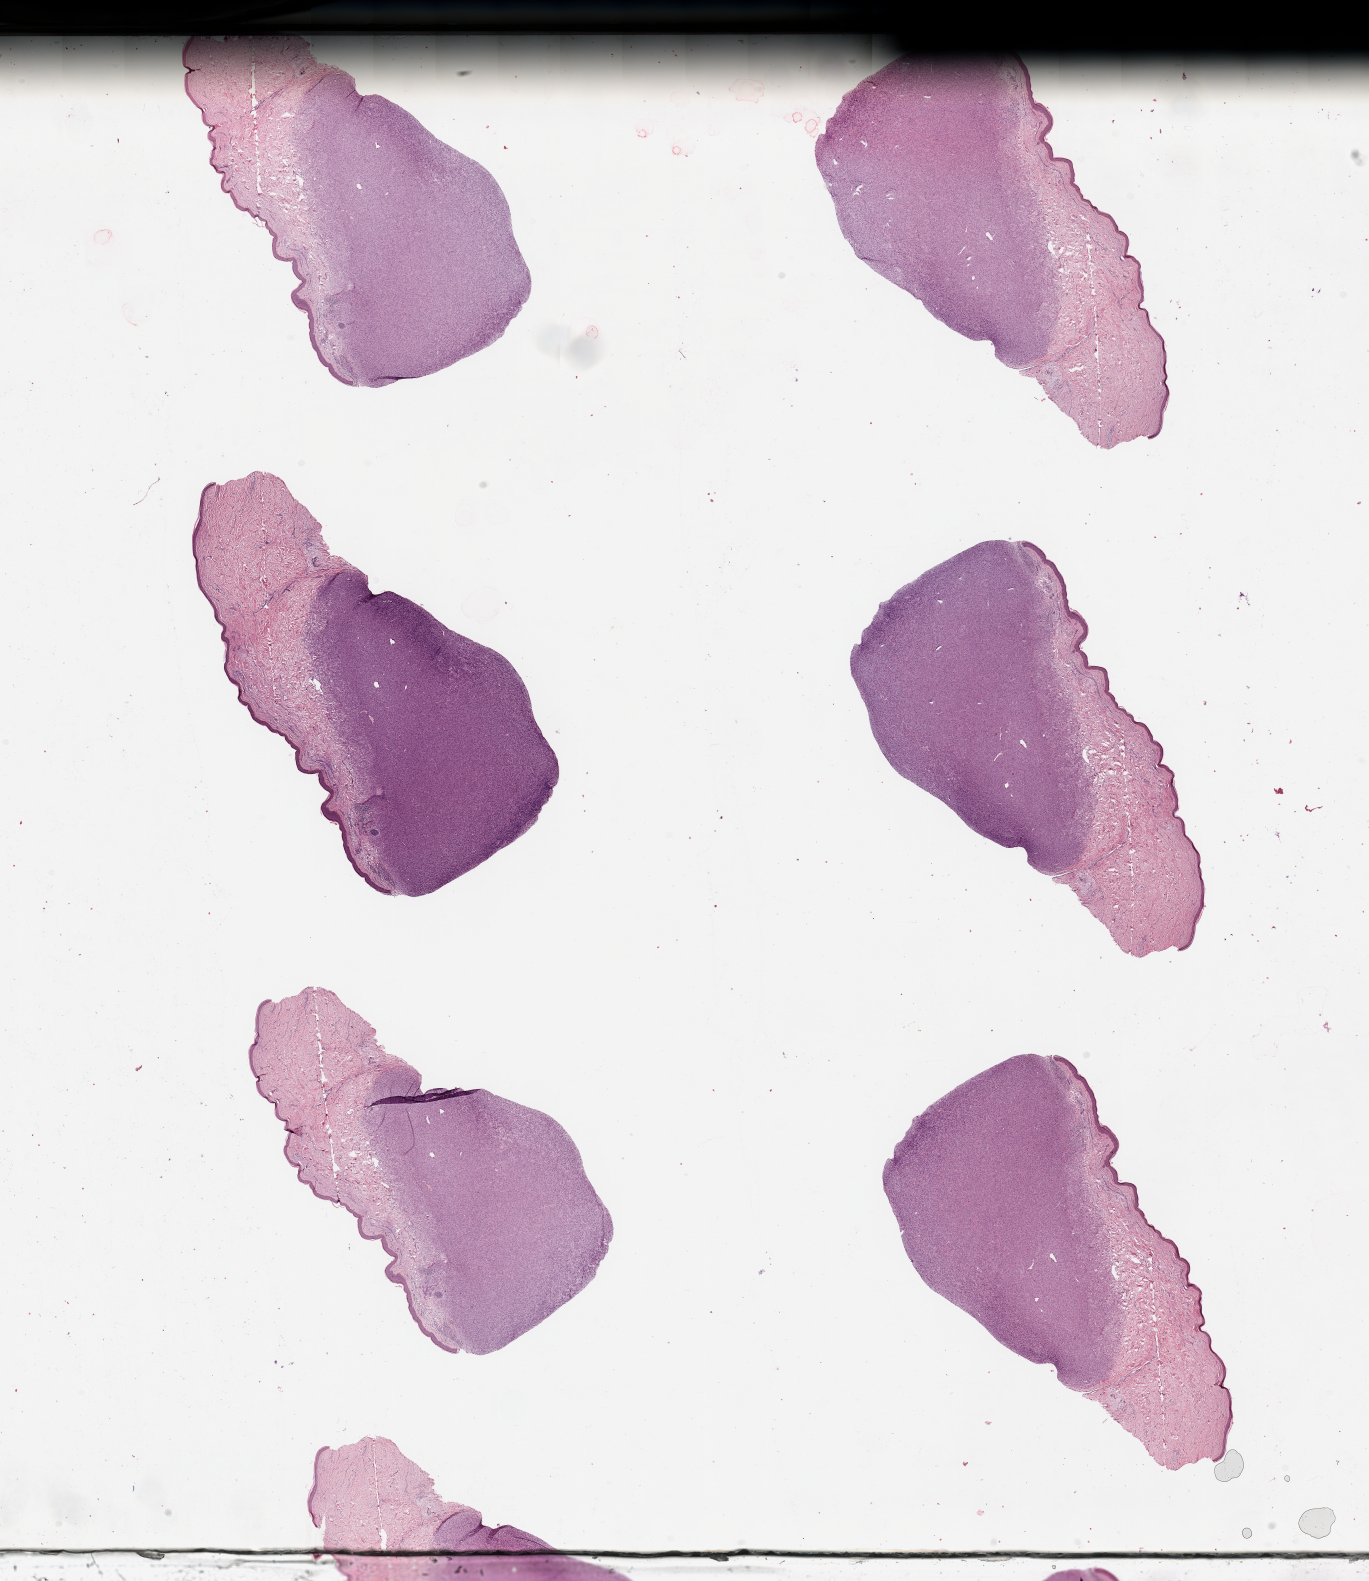
H&E whole-slide image, a low-resolution overview of the entire scanned area, about 21.7 x 25.0 mm (from a 20x scan); tumour tissue sample. Male, 68 y/o.
Patient diagnosis (cohort enrolment): sarcoma (site not recorded at cohort level).